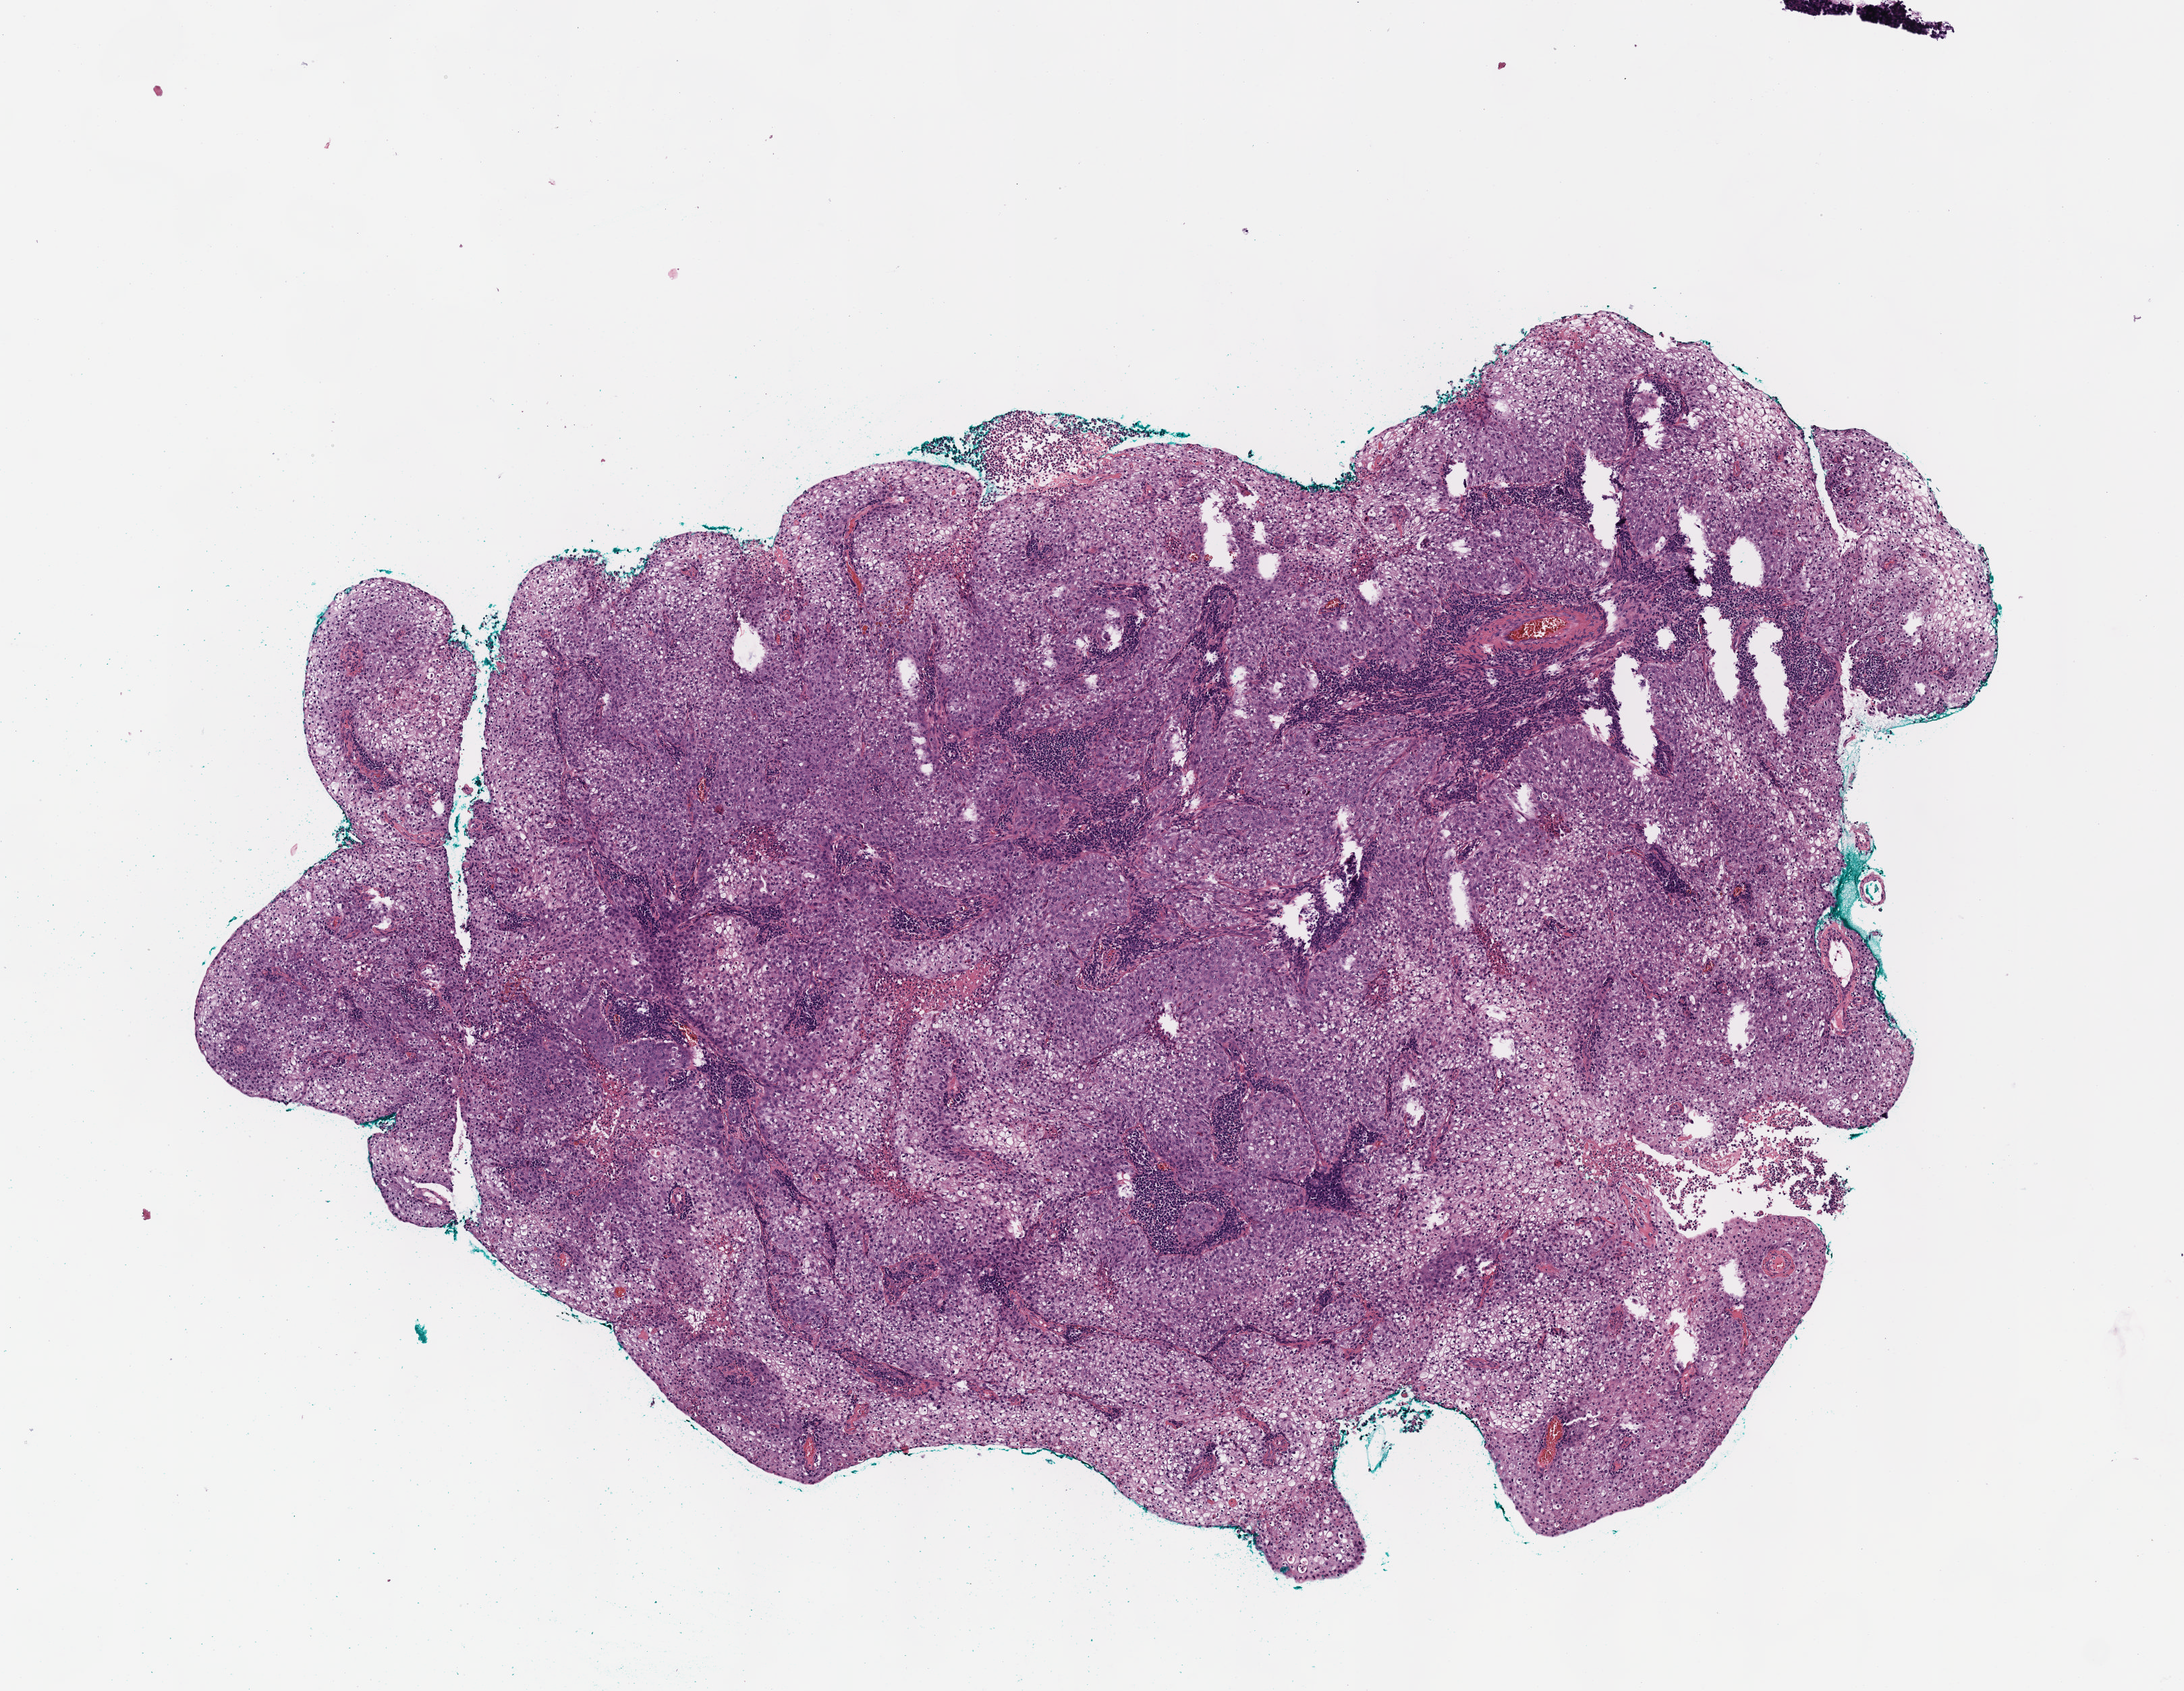
Hematoxylin and eosin (H&E) stained whole-slide image, shown as a low-resolution overview of the whole scanned area (about 6.5 x 5.1 mm, from a 40x scan), formalin-fixed paraffin-embedded (FFPE) diagnostic section, primary tumour sample from the cervix. Female, age 51 years at initial diagnosis.
Diagnosis: Squamous cell carcinoma, NOS (cervix uteri).